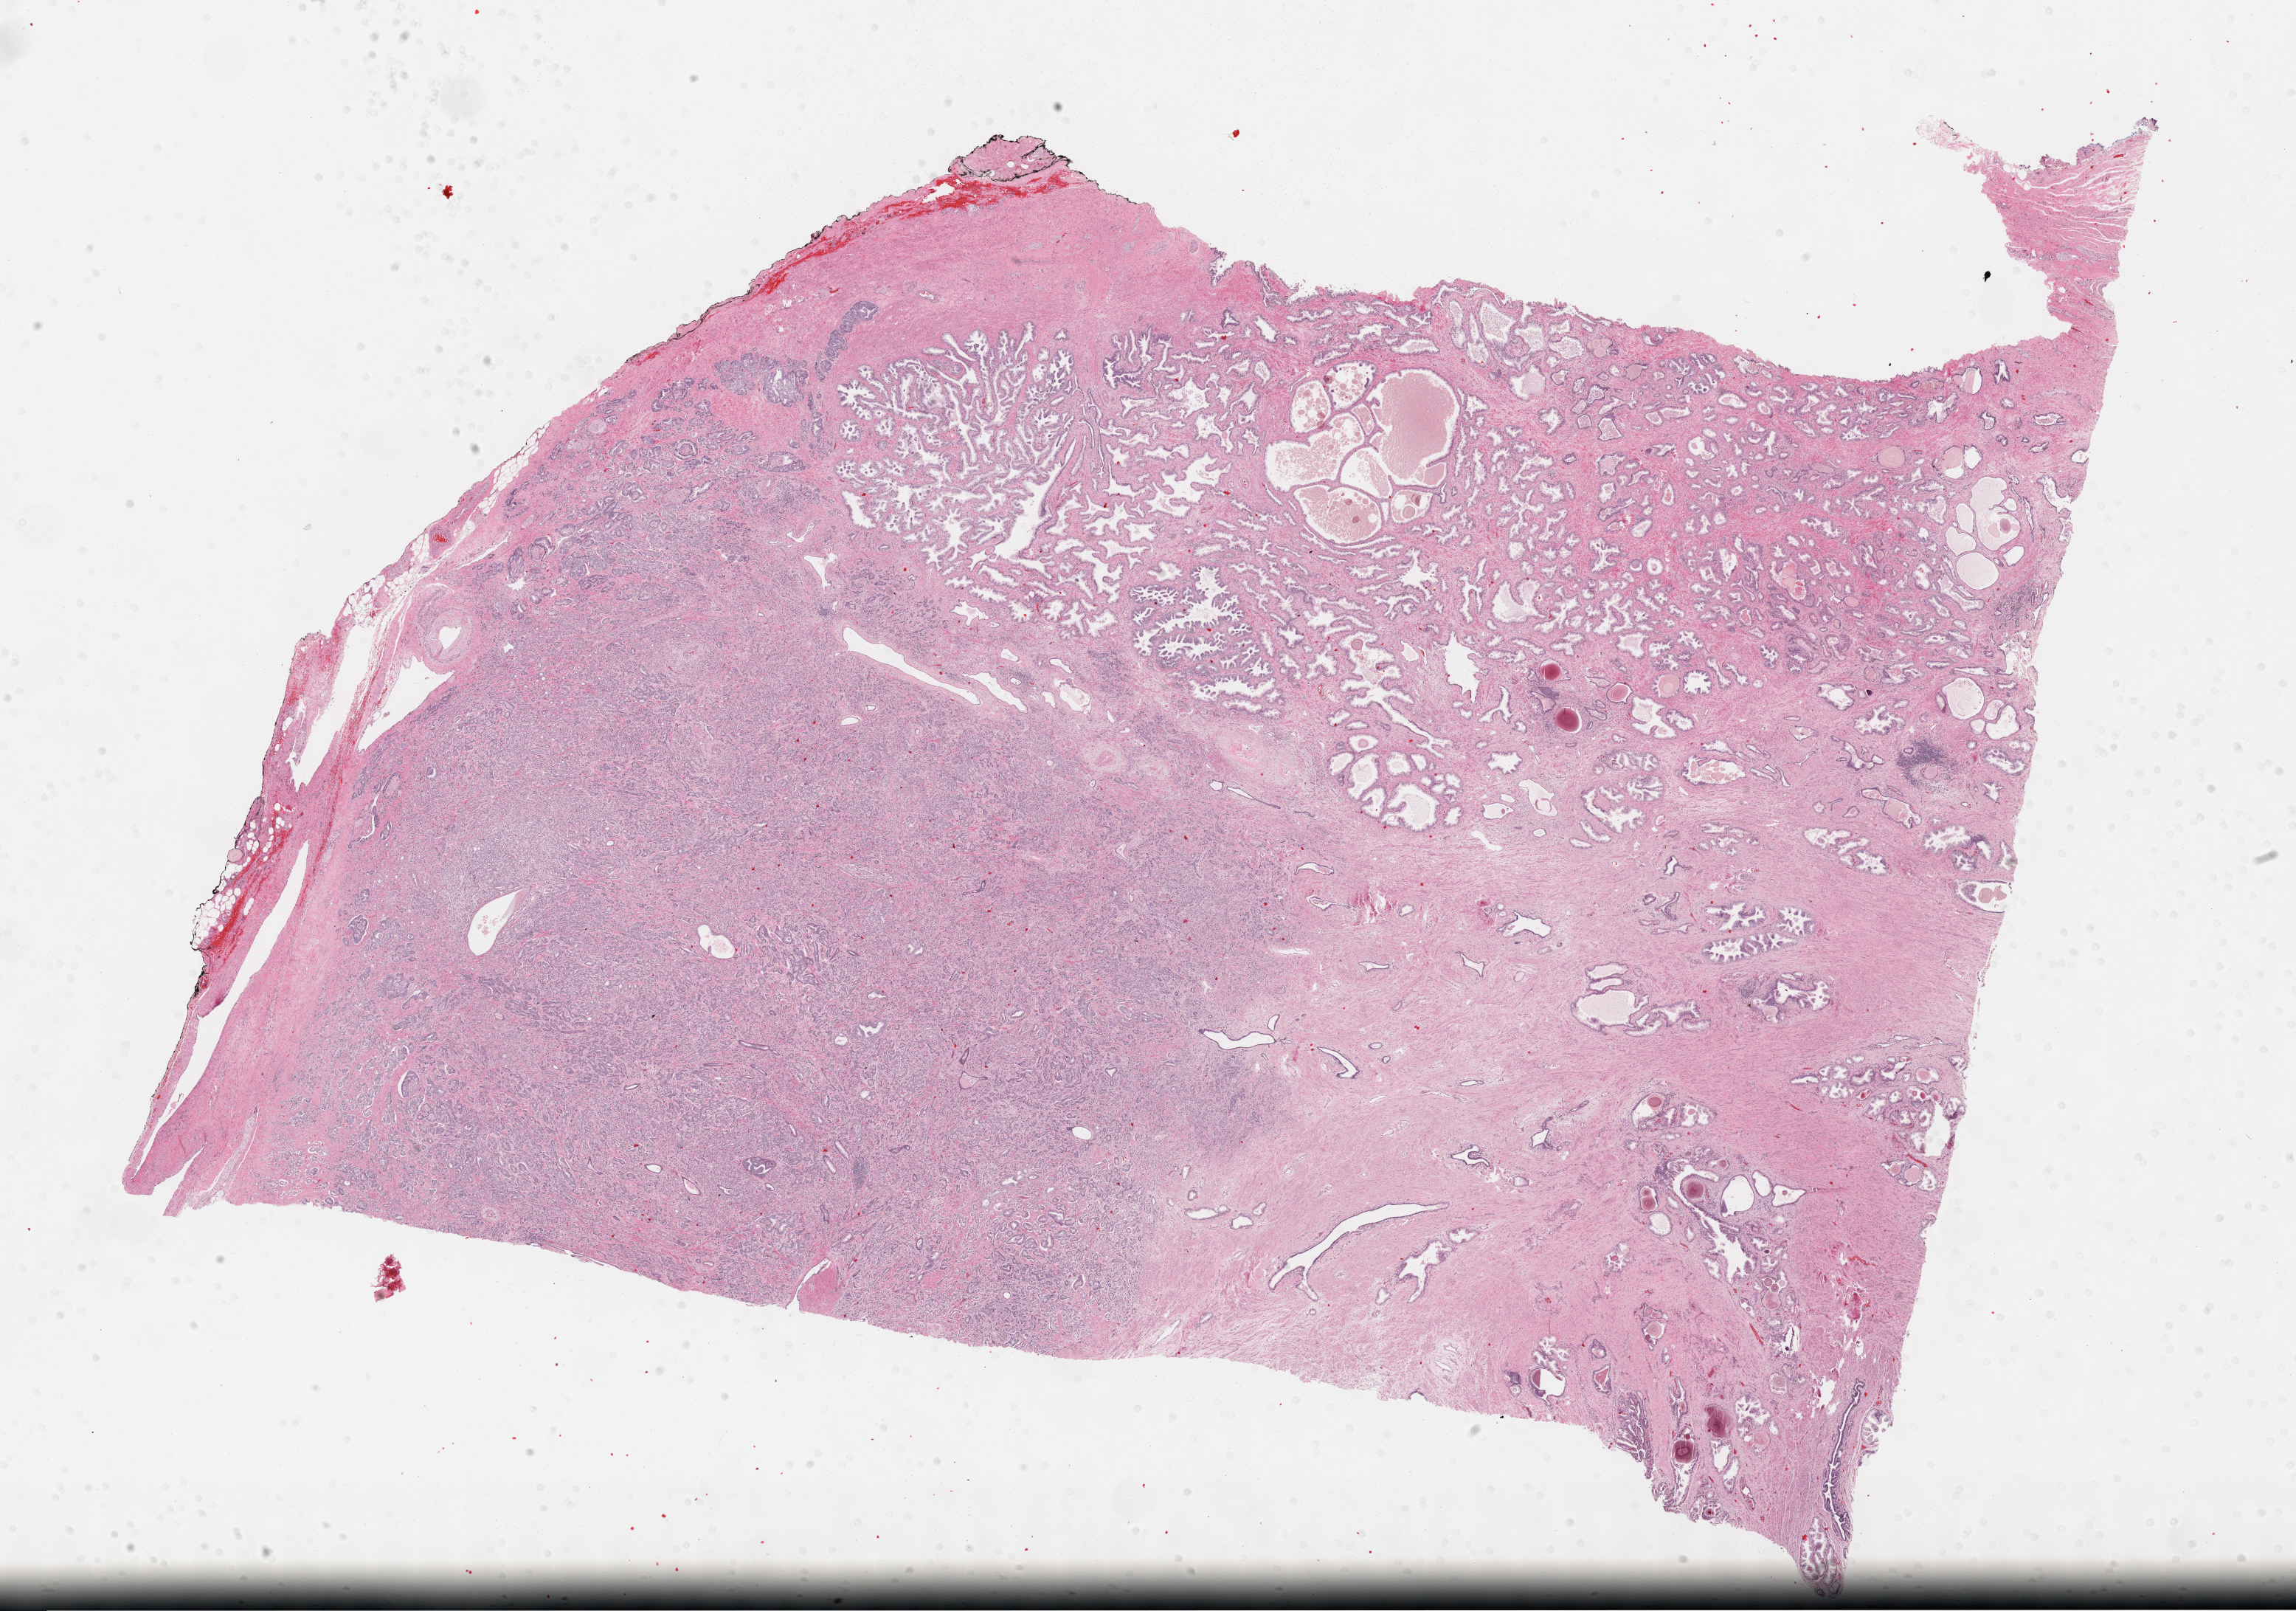
H&E whole-slide image, a low-resolution overview of the entire scanned area, about 25.2 x 17.7 mm; FFPE section; prostate, primary tumour sample. Patient: male, age at initial diagnosis 65 years. Gleason score: 9 (4+5).
* laterality: right
* histologic diagnosis: Adenocarcinoma, NOS
* lymph nodes positive (case pathology): 0 of 3 examined